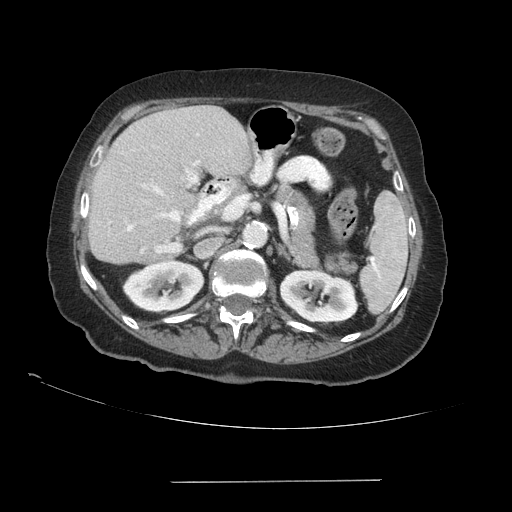
Contrast-enhanced abdominal CT (liver protocol), one axial slice. Slice 51 of 89 in the series (ordered by position). 140 kVp. Soft-tissue window (W 400 / L 40 HU). 2.5 mm slice thickness. 512 × 512 image matrix. From the clinical record (not read from this slice): diagnosis: hepatocellular carcinoma (patient treated with transarterial chemoembolisation; whether this scan precedes or follows treatment is not stated here); TNM stage (as recorded): Stage-IVA; Child-Pugh class: A; tumour differentiation: poorly differentiated; tumour nodularity: uninodular.
Outlined on this slice (semi-automatic segmentation, software-assisted and operator-edited):
- liver parenchyma outside the tumour (the mass and vessels are separate outlines, so this box may not span the whole liver): bounding box <88,106,250,264> (left, top, right, bottom; pixels)
- liver vessels: <127,133,199,252>